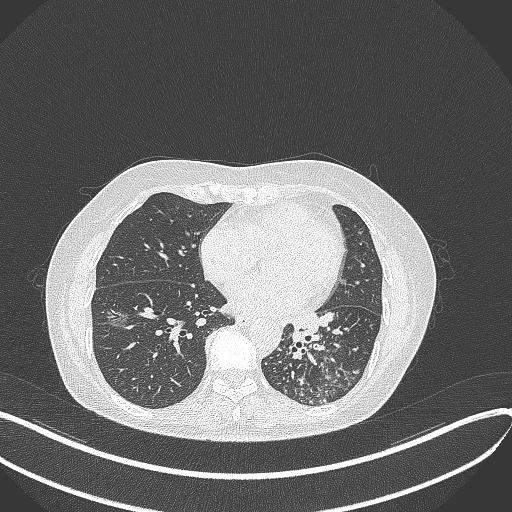
Chest CT, one axial slice. 100 kVp. Lung window (W 1500 / L -600 HU). 1 mm slice thickness. 512 × 512 image matrix, field of view 400 × 400 mm. Patient: female, 63 years. Case-level facts recorded for this patient, not image findings: clinical TNM (as recorded): T1b N0 M0.
Structures marked on this image (bounding box drawn by a radiologist):
- lung tumour (recorded histology: adenocarcinoma): bounding box [x1, y1, x2, y2] px = [287, 309, 324, 347]